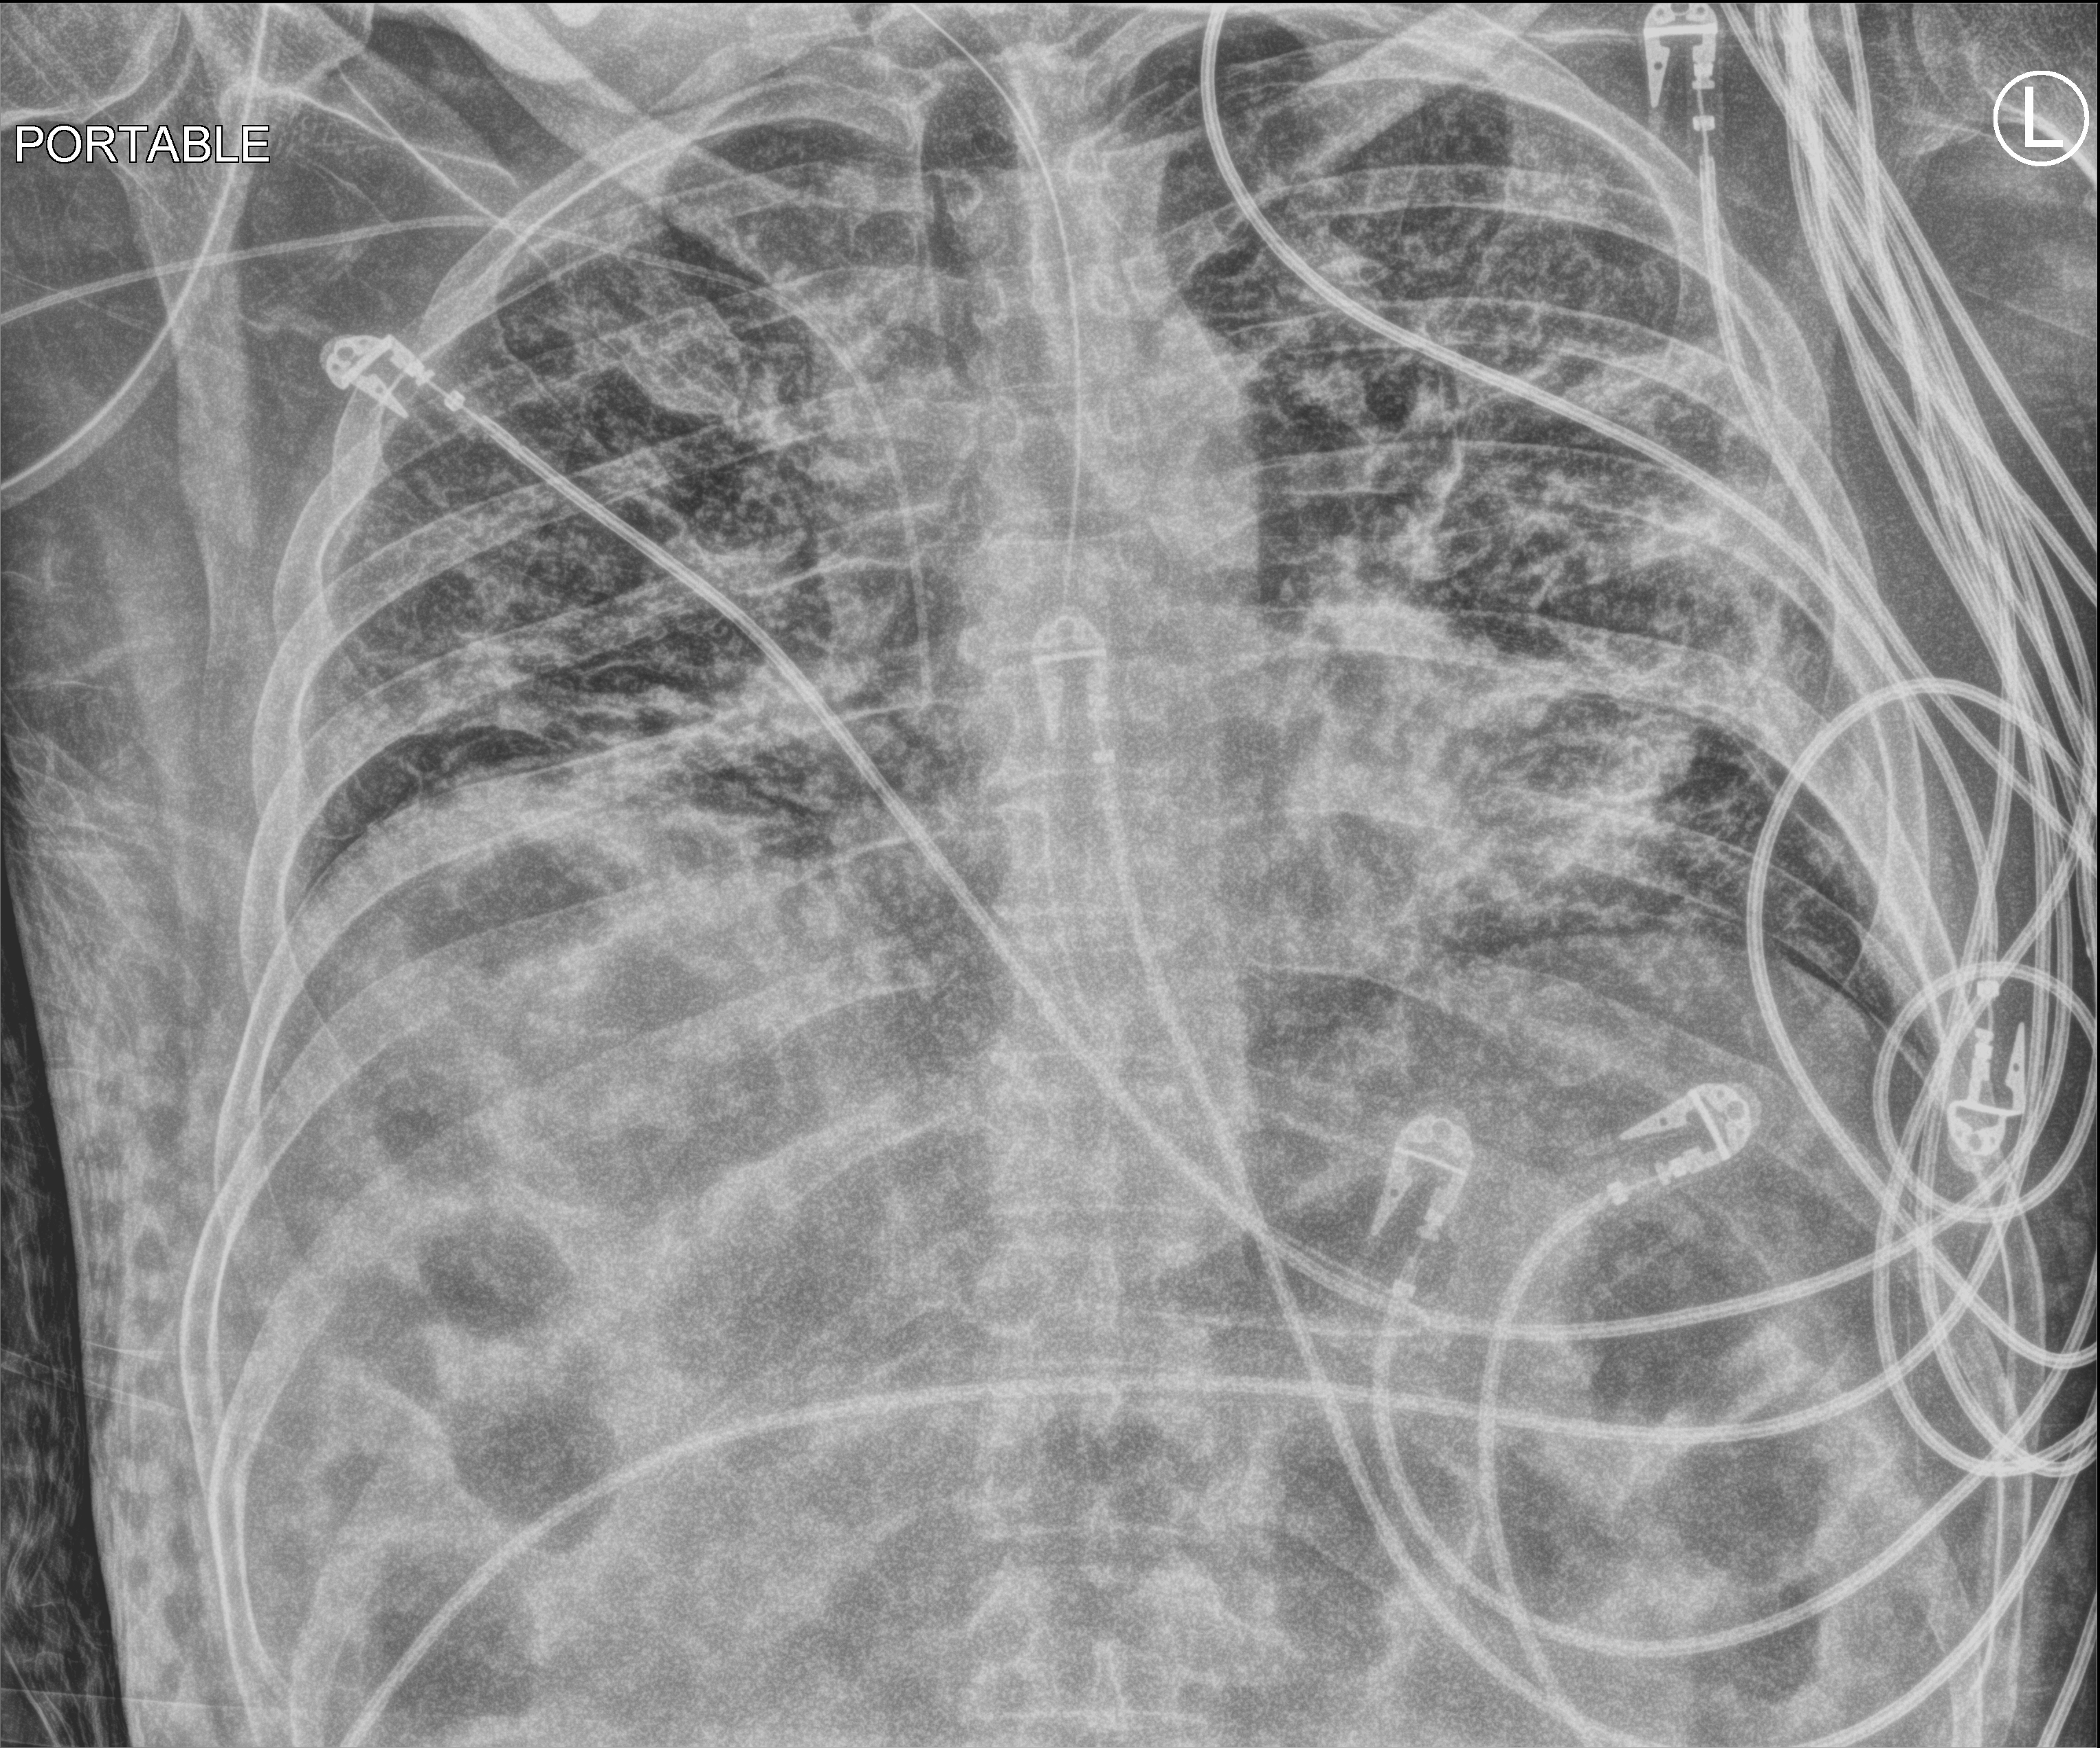
Bedside chest radiograph (computed radiography); anteroposterior (AP) projection. Patient hospitalised with COVID-19; male, aged 18–59 years.
From the hospital-stay record, not from the radiograph (when in the stay this image was taken is not recorded): other chronic lung disease (admission record): no; diabetes (admission record): no.